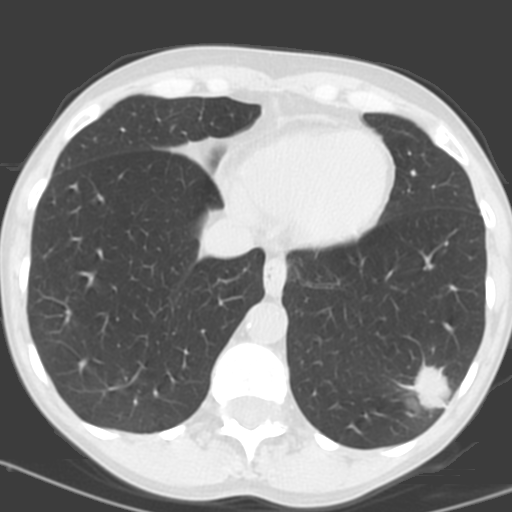
Low-dose screening chest CT, one axial slice; slice 44 of 156 in the series (ordered by position); 120 kVp; lung window (W 1500 / L -600 HU); 3.2 mm slice thickness; 512 × 512 image matrix, field of view 262 × 262 mm.
Outlined on this slice (outlined manually by an expert reader):
- lesion 1 (tumor, lower lobe of left lung): bounding box (x1, y1, x2, y2) in pixels: (415, 365, 452, 410)